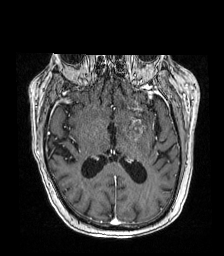
Brain MRI from a brain-tumour surgery series, one axial slice; position 88 of 192 along the scan axis; T1-weighted post-contrast; 1 mm slice thickness; 224 × 256 image matrix, field of view 219 × 250 mm. From the clinical record (not read from this slice): histopathology: Metastatic carcinoma from lung primary.
Annotated regions visible in this slice (expert manual segmentation):
- tumour: bounding box <117,115,148,137> (left, top, right, bottom; pixels)